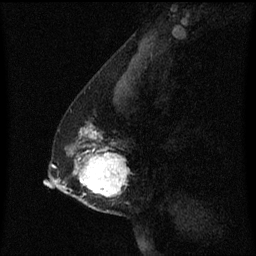
Breast MRI (dynamic contrast-enhanced), one sagittal slice; dynamic contrast-enhanced series, image 2 of 3 at this slice position (ordered by acquisition); 1.5 T; TE 4.2 ms, TR 8.4 ms; 2 mm slice thickness; 256 × 256 image matrix, field of view 200 × 200 mm. Patient: female, 40 years. Case-level facts recorded for this patient, not image findings: setting: breast cancer imaged before/during neoadjuvant chemotherapy; receptor status: triple-negative.
Structures marked on this image (semi-automatic segmentation, software-assisted and operator-edited):
- analysis volume of interest (the breast-tissue region the enhancement analysis was run in; not a lesion): bounding box <60,122,131,215> (left, top, right, bottom; pixels)
- tumour enhancement mask (voxels above the 70 % enhancement threshold inside the analysis volume of interest): <78,130,129,197>